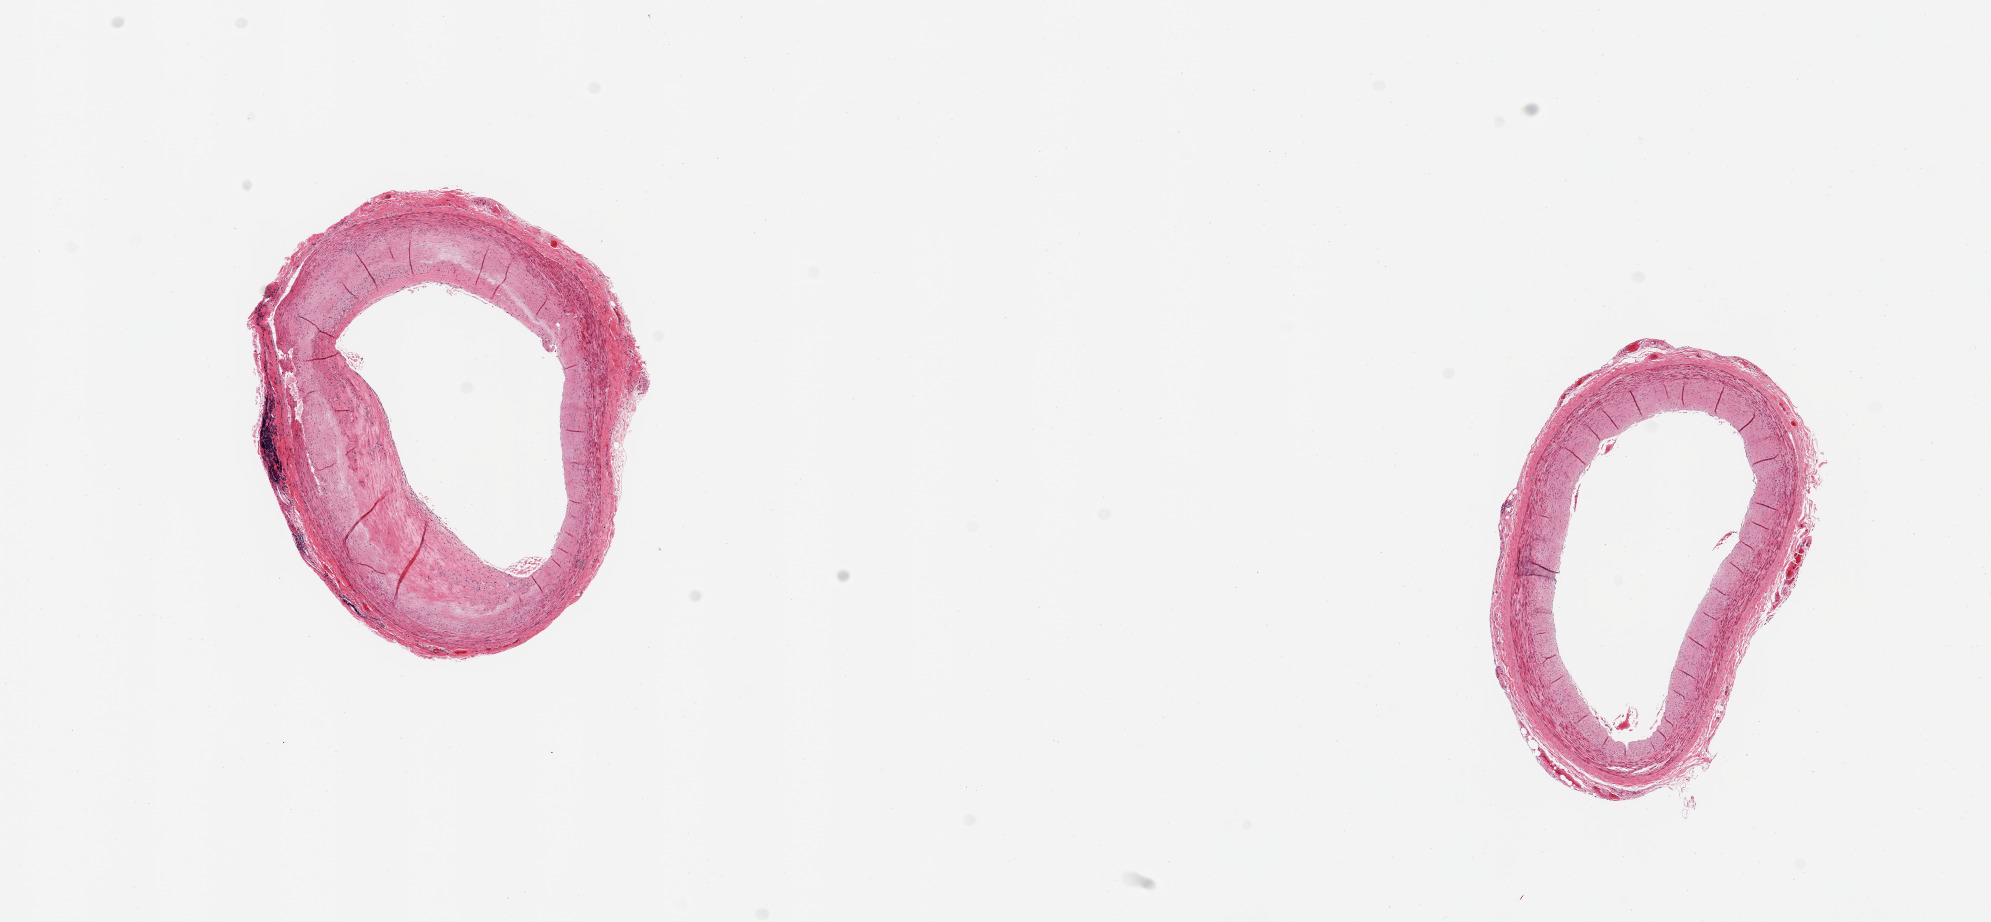
Digitized H&E-stained section, brightfield, low-resolution overview of the scanned area, about 15.8 x 7.3 mm; PAXgene-fixed paraffin-embedded (PFPE) section; section of coronary artery (target tissue); donor tissue sample. Donor sex: male.
* reviewer comment on this tissue sample: 2 pieces, ~20% occlusive atherosis